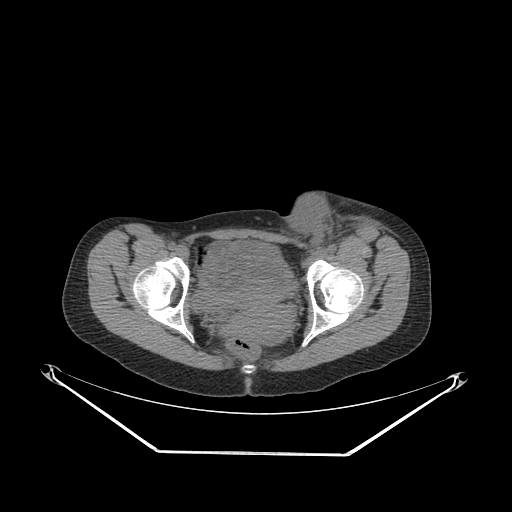
CT of an extremity soft-tissue mass (from a PET/CT study), one axial slice; position 73 of 267 along the scan axis; reconstruction kernel SOFT; 140 kVp; soft-tissue window (W 400 / L 40 HU); 512 × 512 image matrix, field of view 500 × 500 mm. Female patient. Case-level facts recorded for this patient, not image findings: histological type: leiomyosarcoma; grade: high; site of the primary tumour: groin.
Structures marked on this image (expert contour drawn on MRI and transferred to this co-registered scan by the dataset authors):
- gross tumour volume including surrounding oedema: bounding box <279,196,387,261> (left, top, right, bottom; pixels)
- gross tumour volume (mass): <281,196,339,252>